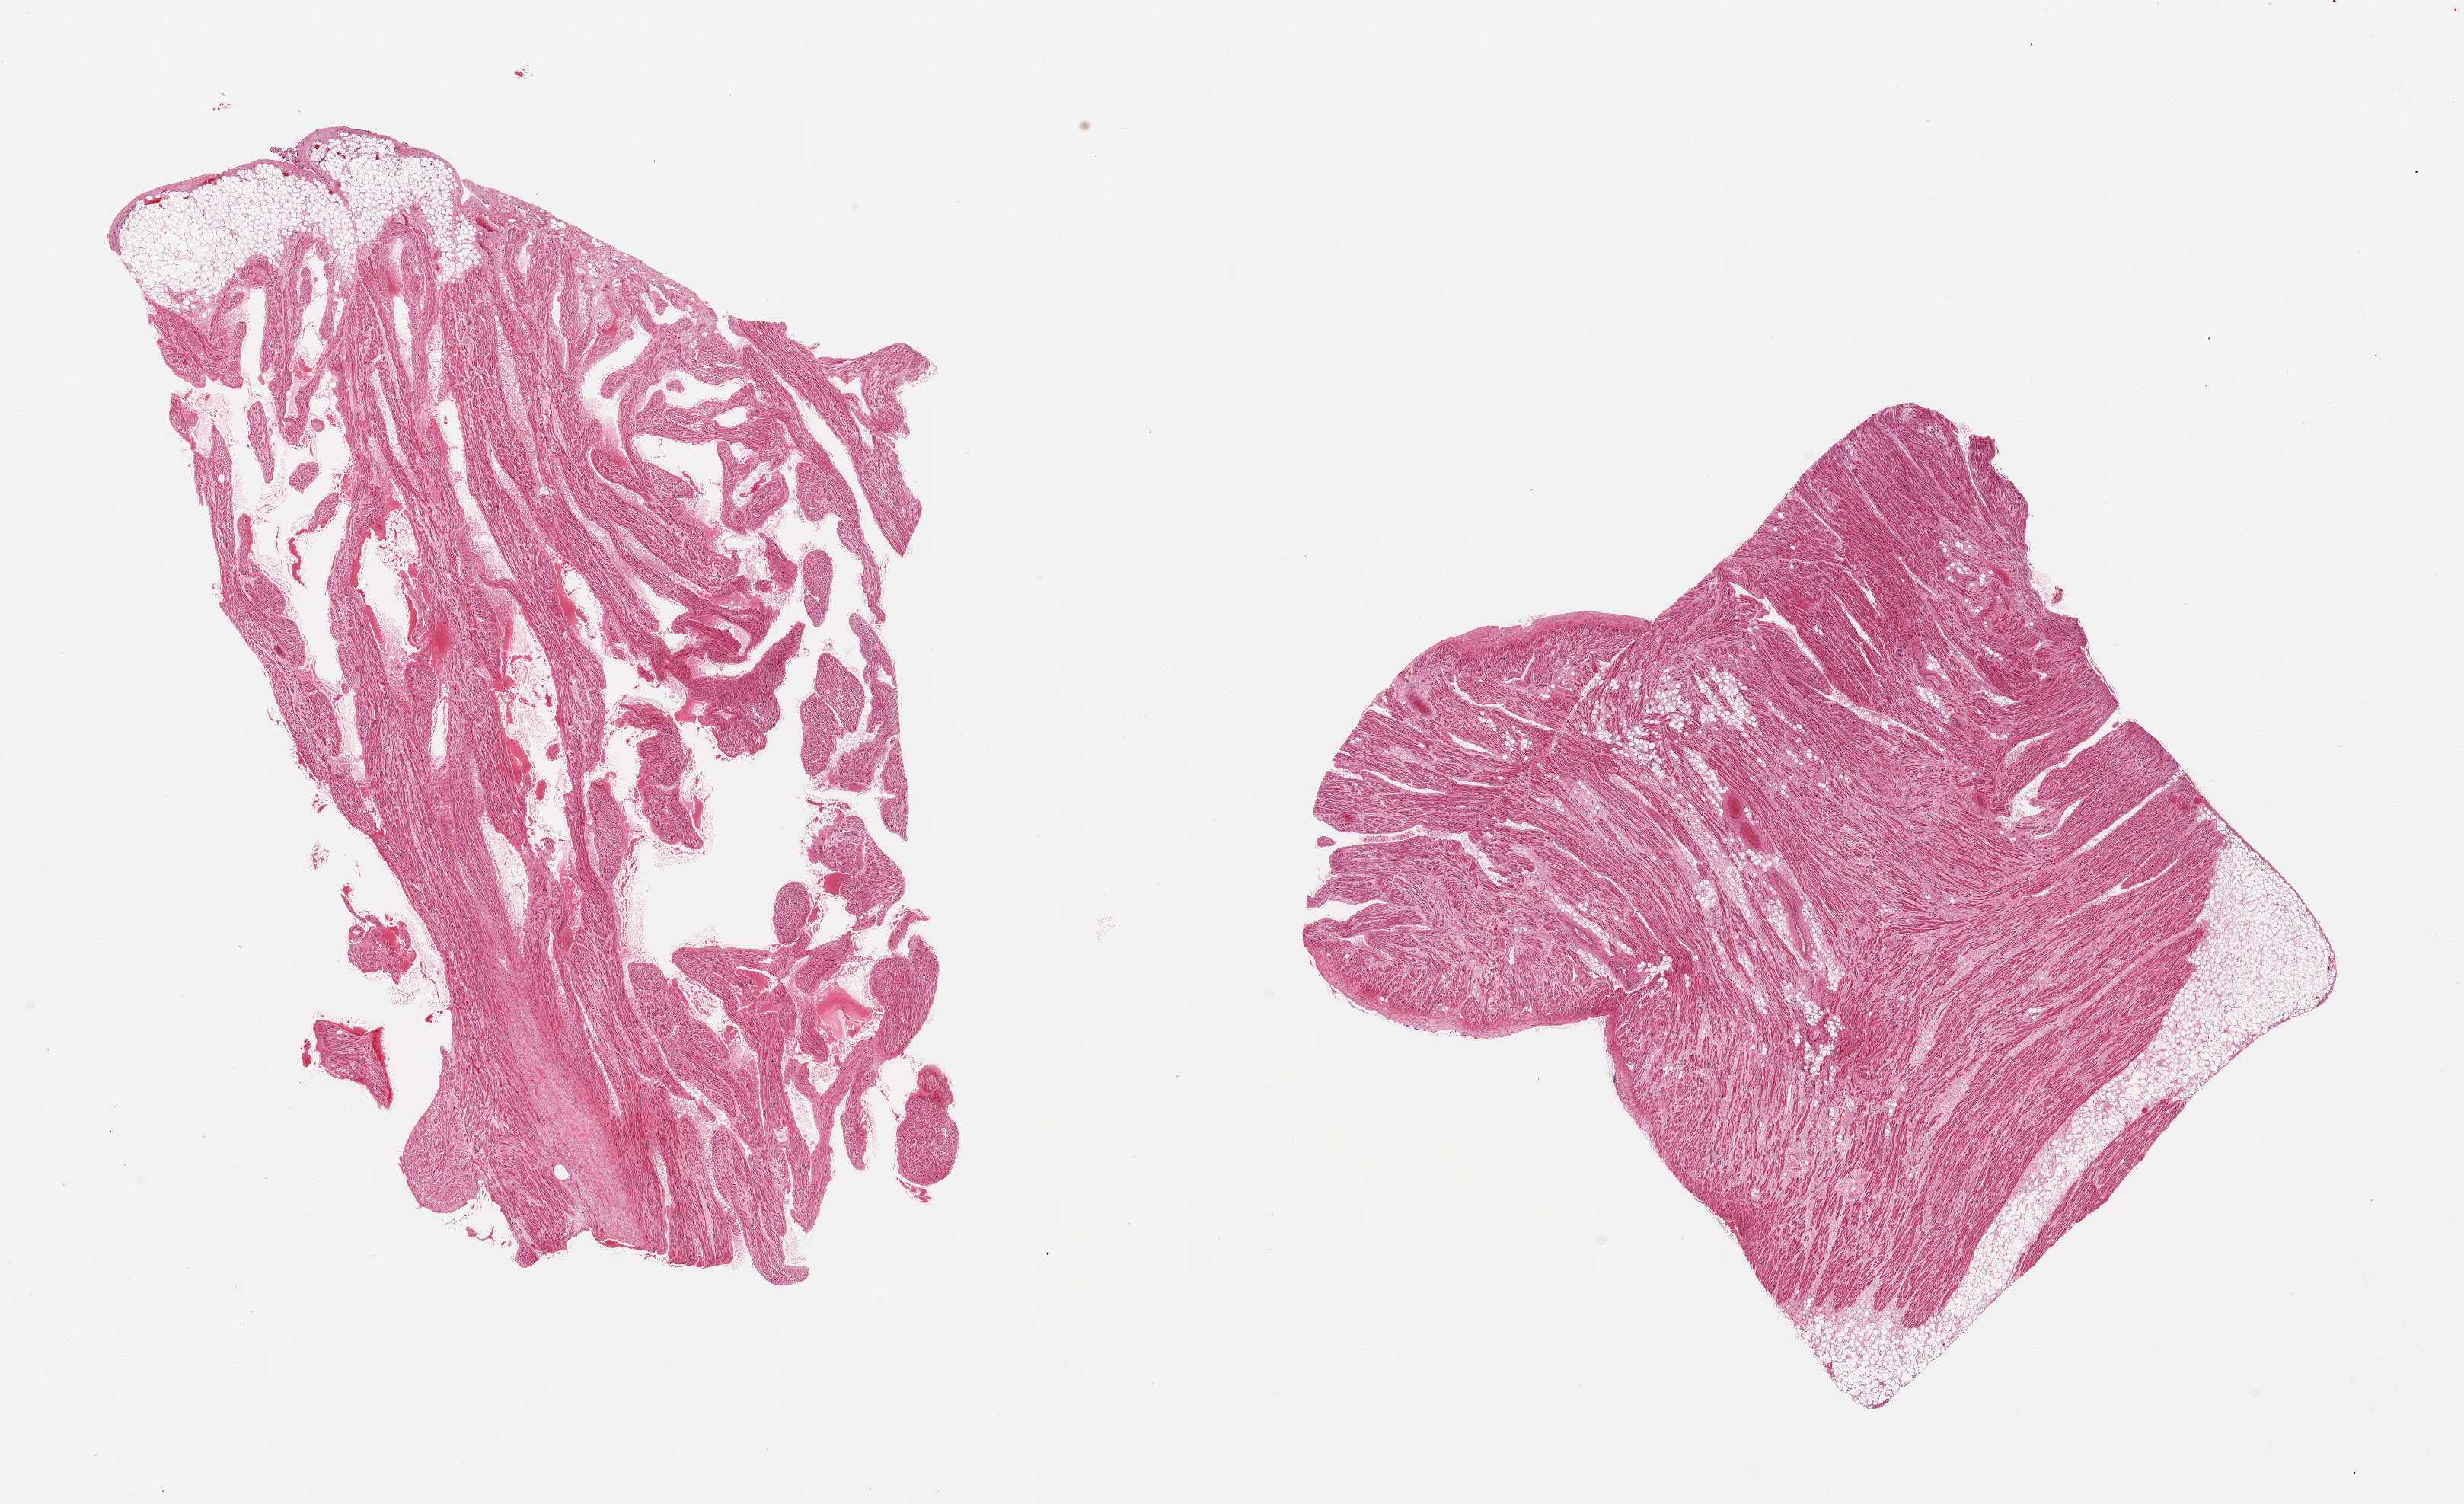
Whole-slide image, hematoxylin and eosin (H&E) stain, shown as a low-resolution overview of the whole scanned area (about 25.6 x 15.6 mm). PAXgene-fixed, paraffin-embedded tissue. Section of auricular appendage (target tissue). Tissue donor sample. Donor sex: male.
Pathologist's review note for this sample: 2 pieces; 10% internal and external fat & fibrous content.